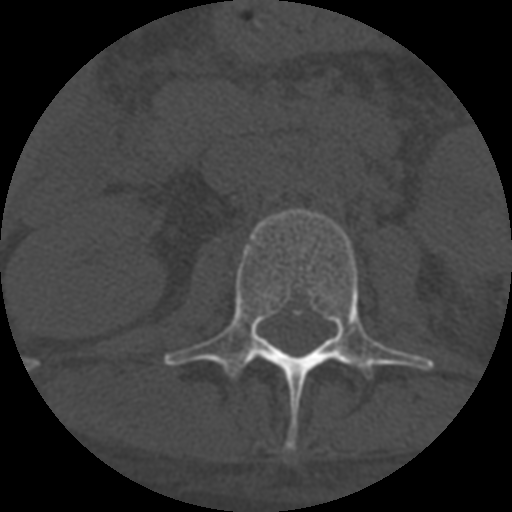
CT including the spine, one axial slice; position 263 of 708 along the scan axis; one of 3 acquisitions stored at this slice position; bone window (W 1800 / L 400 HU); 1.25 mm slice thickness; 512 × 512 image matrix, field of view 160 × 160 mm. Patient age 55 years. Case-level facts recorded for this patient, not image findings: primary cancer: colon; vertebrae with lytic lesions (as recorded): T12, L1, L5.
Annotated regions visible in this slice (semi-automatically segmented with operator editing):
- L2 vertebra: bounding box <164,209,434,450> (left, top, right, bottom; pixels)